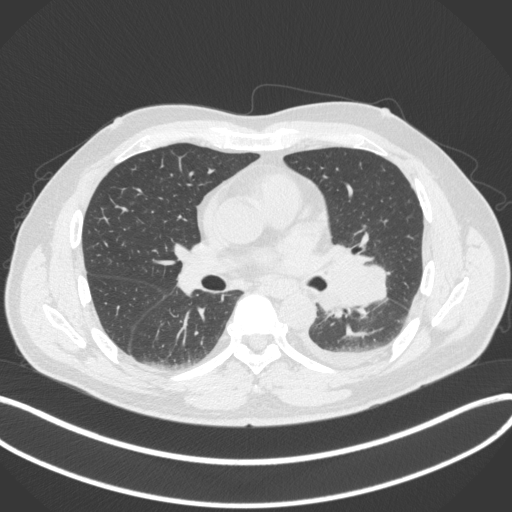
Chest CT, one axial slice. Slice 193 of 350 in the series (ordered by position). Reconstruction kernel B31f. 120 kVp. Lung window (W 1500 / L -600 HU). 512 × 512 image matrix, field of view 400 × 400 mm. Patient: male, 58 years. Case-level facts recorded for this patient, not image findings: clinical TNM (as recorded): T3 N1 M1b.
Outlined on this slice (rectangle marked by the reading radiologist):
- lung tumour (recorded histology: small cell carcinoma): bounding box [x1, y1, x2, y2] px = [319, 243, 391, 318]